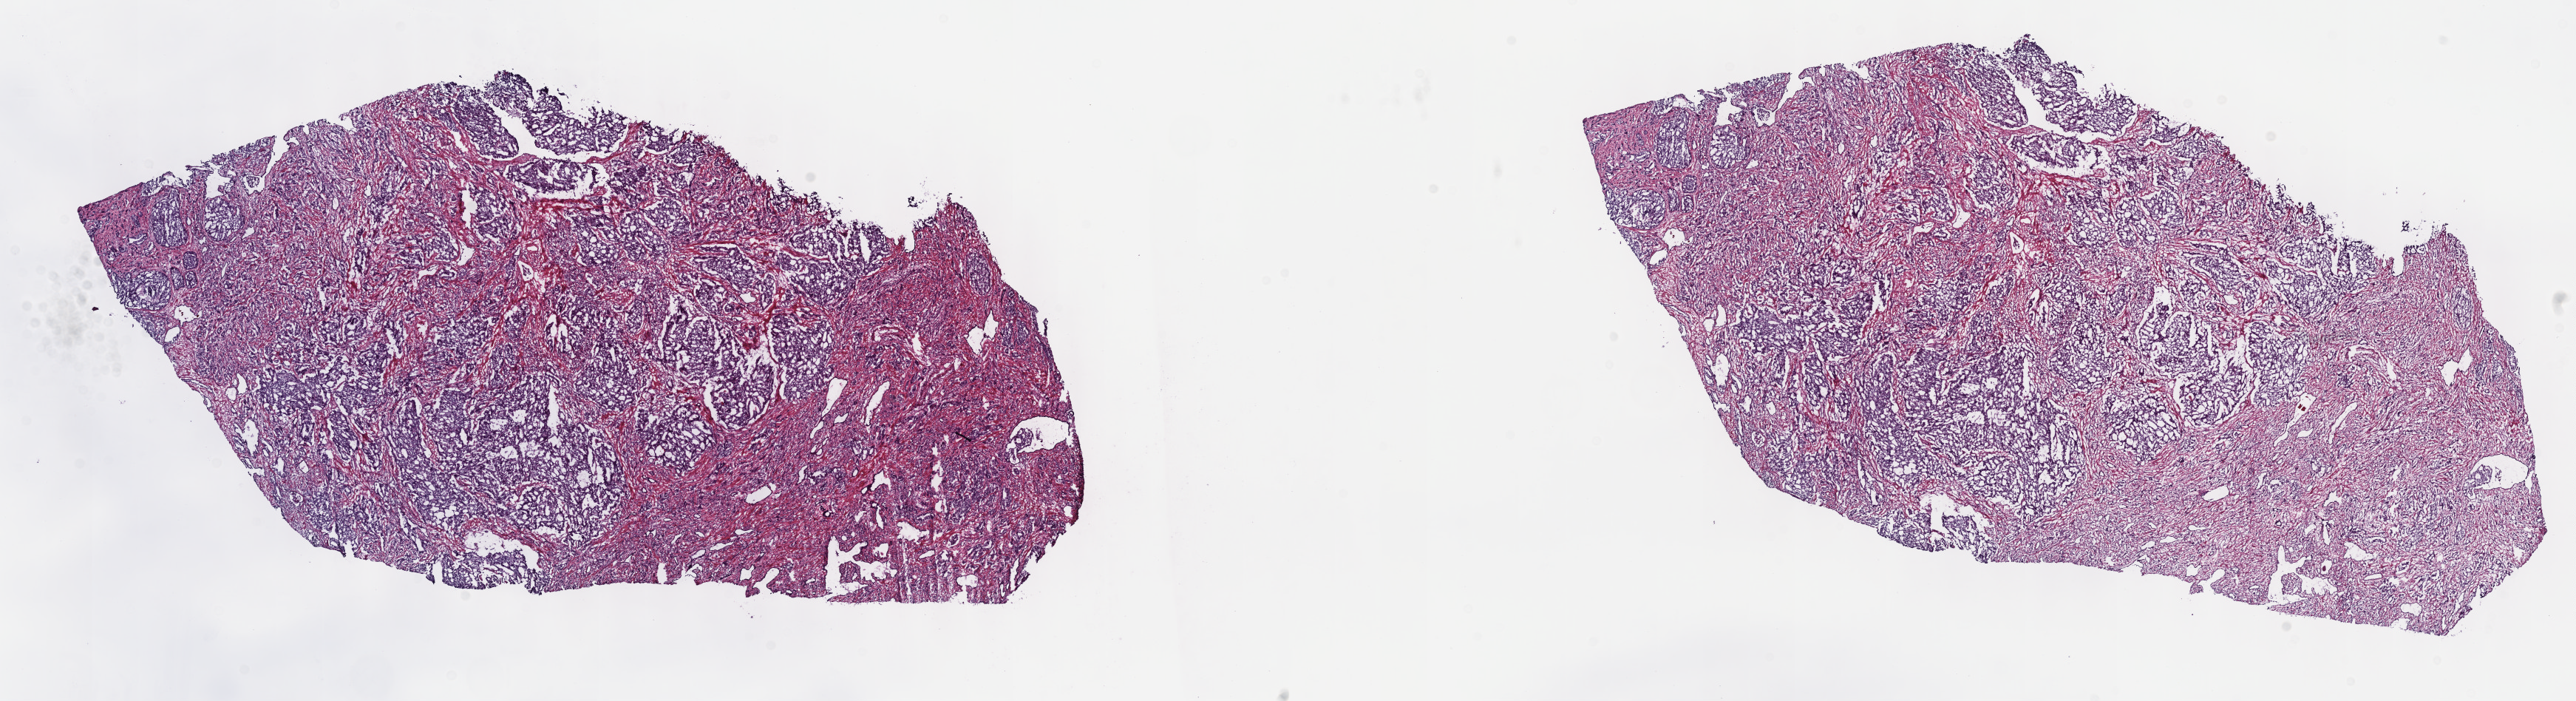
Whole-slide histology image, Hematoxylin and eosin (H&E) stained — whole scanned area (about 28.2 x 7.7 mm) shown as a low-resolution overview, frozen section from the top of the tissue portion, primary tumour sample from the prostate. Male patient; age at initial diagnosis 60 years. Gleason score: 7 (4+3). Pathologist review of this section (percent, as recorded): tumour cells 80%, tumour nuclei 85%, normal cells 10%, stromal cells 10%, necrosis 0%. Infiltration values recorded for this section: lymphocyte infiltration 0%, monocyte infiltration 0%, neutrophil infiltration 0%.
Diagnosis: Adenocarcinoma, NOS (prostate gland).